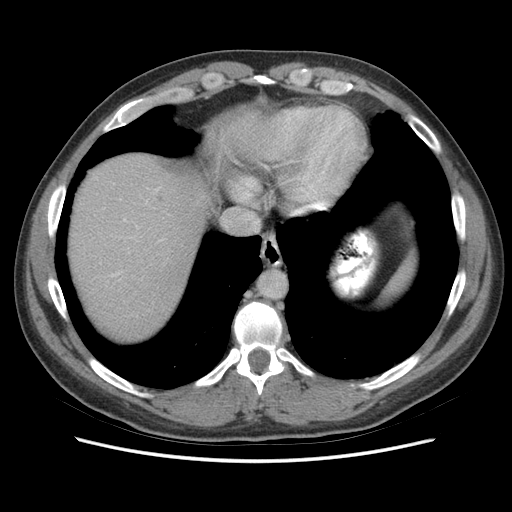
Contrast-enhanced abdominal CT (liver protocol), one axial slice; position 64 of 73 along the scan axis; reconstruction kernel STANDARD; 140 kVp; soft-tissue window (W 400 / L 40 HU); 512 × 512 image matrix, field of view 360 × 360 mm. From the clinical record (not read from this slice): diagnosis: hepatocellular carcinoma (patient treated with transarterial chemoembolisation; whether this scan precedes or follows treatment is not stated here); TNM stage (as recorded): Stage-IIIA.
Outlined on this slice (semi-automatically segmented with operator editing):
- abdominal aorta: box from (x=259, y=272) to (x=287, y=299) px
- liver parenchyma outside the tumour (the mass and vessels are separate outlines, so this box may not span the whole liver): (x=70, y=154)–(x=210, y=338)